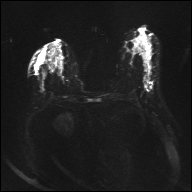
Breast MRI, one axial slice; position 16 of 32 along the scan axis; diffusion-weighted series; image 2 of 4 stored at this slice position (different b-values; order by instance number); 1.5 T; 4 mm slice thickness; 192 × 192 image matrix, field of view 360 × 360 mm. Female patient.
Annotated regions visible in this slice (expert manual segmentation):
- tumour on diffusion-weighted imaging: bounding box <145,78,152,84> (left, top, right, bottom; pixels)